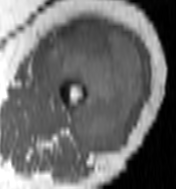
MRI of an extremity soft-tissue mass, one axial slice; slice 63 of 100 in the series (ordered by position); MR volume resampled by the dataset authors to the PET/CT grid (not the native acquisition matrix); 3.27 mm slice thickness; 176 × 189 image matrix, field of view 172 × 185 mm. Female patient. Case-level facts recorded for this patient, not image findings: histological type: undifferentiated – high grade; grade: high; site of the primary tumour: left thigh.
Annotated regions visible in this slice (expert contour drawn on MRI and transferred to this co-registered scan by the dataset authors):
- gross tumour volume including surrounding oedema: bounding box (x1, y1, x2, y2) in pixels: (46, 23, 145, 154)
- gross tumour volume (mass): (46, 23, 143, 154)